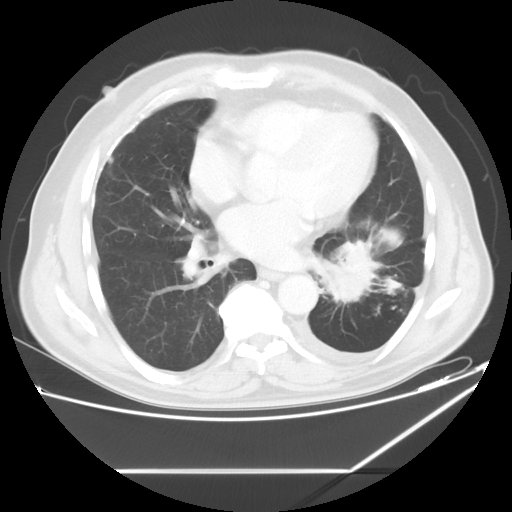
Chest CT, one axial slice; position 27 of 60 along the scan axis; reconstruction kernel STANDARD; 120 kVp; lung window (W 1500 / L -600 HU); 512 × 512 image matrix, field of view 395 × 395 mm. Male patient, age 62 years. Case-level facts recorded for this patient, not image findings: clinical TNM (as recorded): T3 N0 M1.
Annotated regions visible in this slice (rectangle marked by the reading radiologist):
- lung tumour (recorded histology: adenocarcinoma): bounding box (x1, y1, x2, y2) in pixels: (325, 228, 378, 300)
- lung tumour (recorded histology: adenocarcinoma): (326, 234, 382, 304)